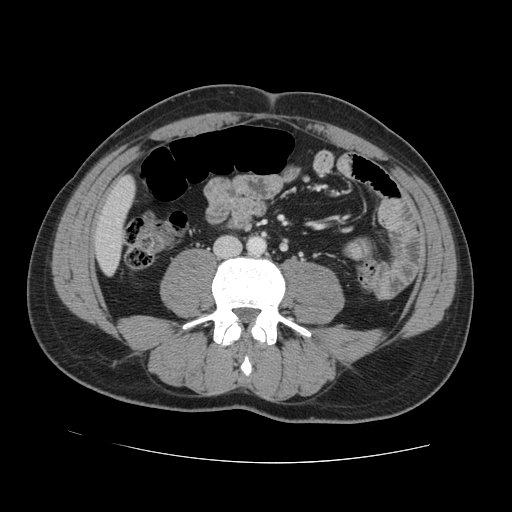
Contrast-enhanced abdominal CT, one axial slice; slice 16 of 131 in the series (ordered by position); 120 kVp; intravenous contrast given; soft-tissue window (W 400 / L 40 HU); 2.5 mm slice thickness; 512 × 512 image matrix, field of view 380 × 380 mm. Male patient, age 40 years. From the clinical record (not read from this slice): diagnosis: colorectal cancer liver metastases, imaged before liver resection; multiple liver metastases: yes; largest metastasis: 2.9 cm; chemotherapy before resection: yes.
Outlined on this slice (outlined manually by an expert reader):
- liver: bounding box (x1, y1, x2, y2) in pixels: (95, 179, 134, 273)